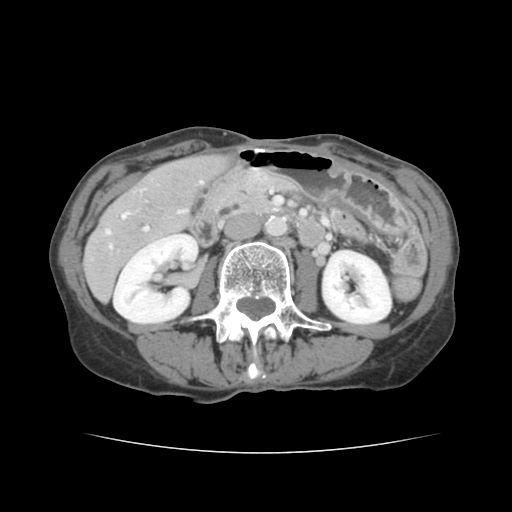
Contrast-enhanced abdominal CT, one axial slice. Slice 49 of 136 in the series (ordered by position). Intravenous contrast given. Soft-tissue window (W 400 / L 40 HU). 512 × 512 image matrix, field of view 319 × 319 mm. Female patient, age 77 years. Case-level facts recorded for this patient, not image findings: diagnosis: colorectal cancer liver metastases, imaged before liver resection; multiple liver metastases: yes; largest metastasis: 3 cm; disease in both lobes: no.
Outlined on this slice (expert manual segmentation):
- hepatic veins: bounding box <106,181,203,248> (left, top, right, bottom; pixels)
- liver: <86,155,222,300>
- planned liver remnant (the part of the liver to remain after resection): <170,156,223,193>
- portal vein (with intrahepatic branches): <144,211,181,231>